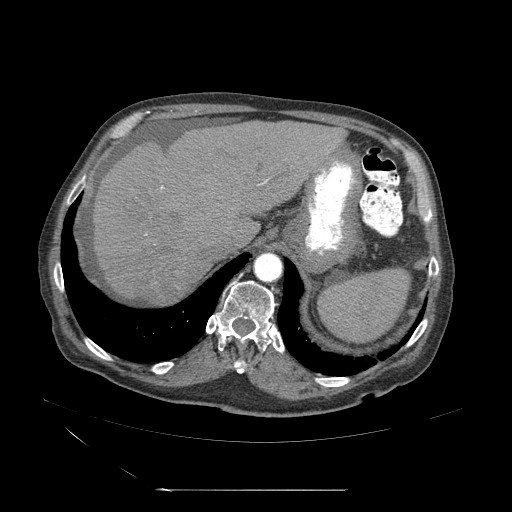
Contrast-enhanced abdominal CT (liver protocol), one axial slice; 120 kVp; soft-tissue window (W 400 / L 40 HU); 512 × 512 image matrix, field of view 440 × 440 mm. From the clinical record (not read from this slice): diagnosis: hepatocellular carcinoma (patient treated with transarterial chemoembolisation; whether this scan precedes or follows treatment is not stated here); TNM stage (as recorded): Stage-II.
Annotated regions visible in this slice (semi-automatically segmented with operator editing):
- abdominal aorta: box from (x=254, y=254) to (x=284, y=284) px
- liver parenchyma outside the tumour (the mass and vessels are separate outlines, so this box may not span the whole liver): (x=88, y=121)–(x=348, y=311)
- mass: (x=152, y=271)–(x=190, y=309)
- liver vessels: (x=124, y=199)–(x=231, y=266)